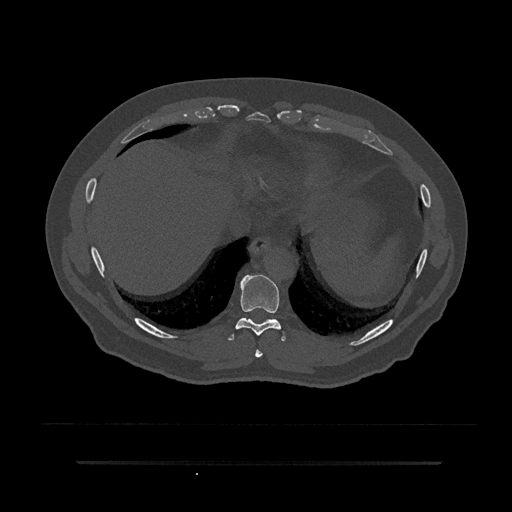
CT including the spine, one axial slice; position 373 of 797 along the scan axis; 120 kVp; bone window (W 1800 / L 400 HU); 0.5 mm slice thickness; 512 × 512 image matrix, field of view 464 × 464 mm. Patient: male, 59 years. From the clinical record (not read from this slice): primary cancer: bile ducts.
Outlined on this slice (semi-automatically segmented with operator editing):
- T8 vertebra: bounding box [x1, y1, x2, y2] px = [255, 349, 263, 357]
- T9 vertebra: [228, 275, 286, 342]